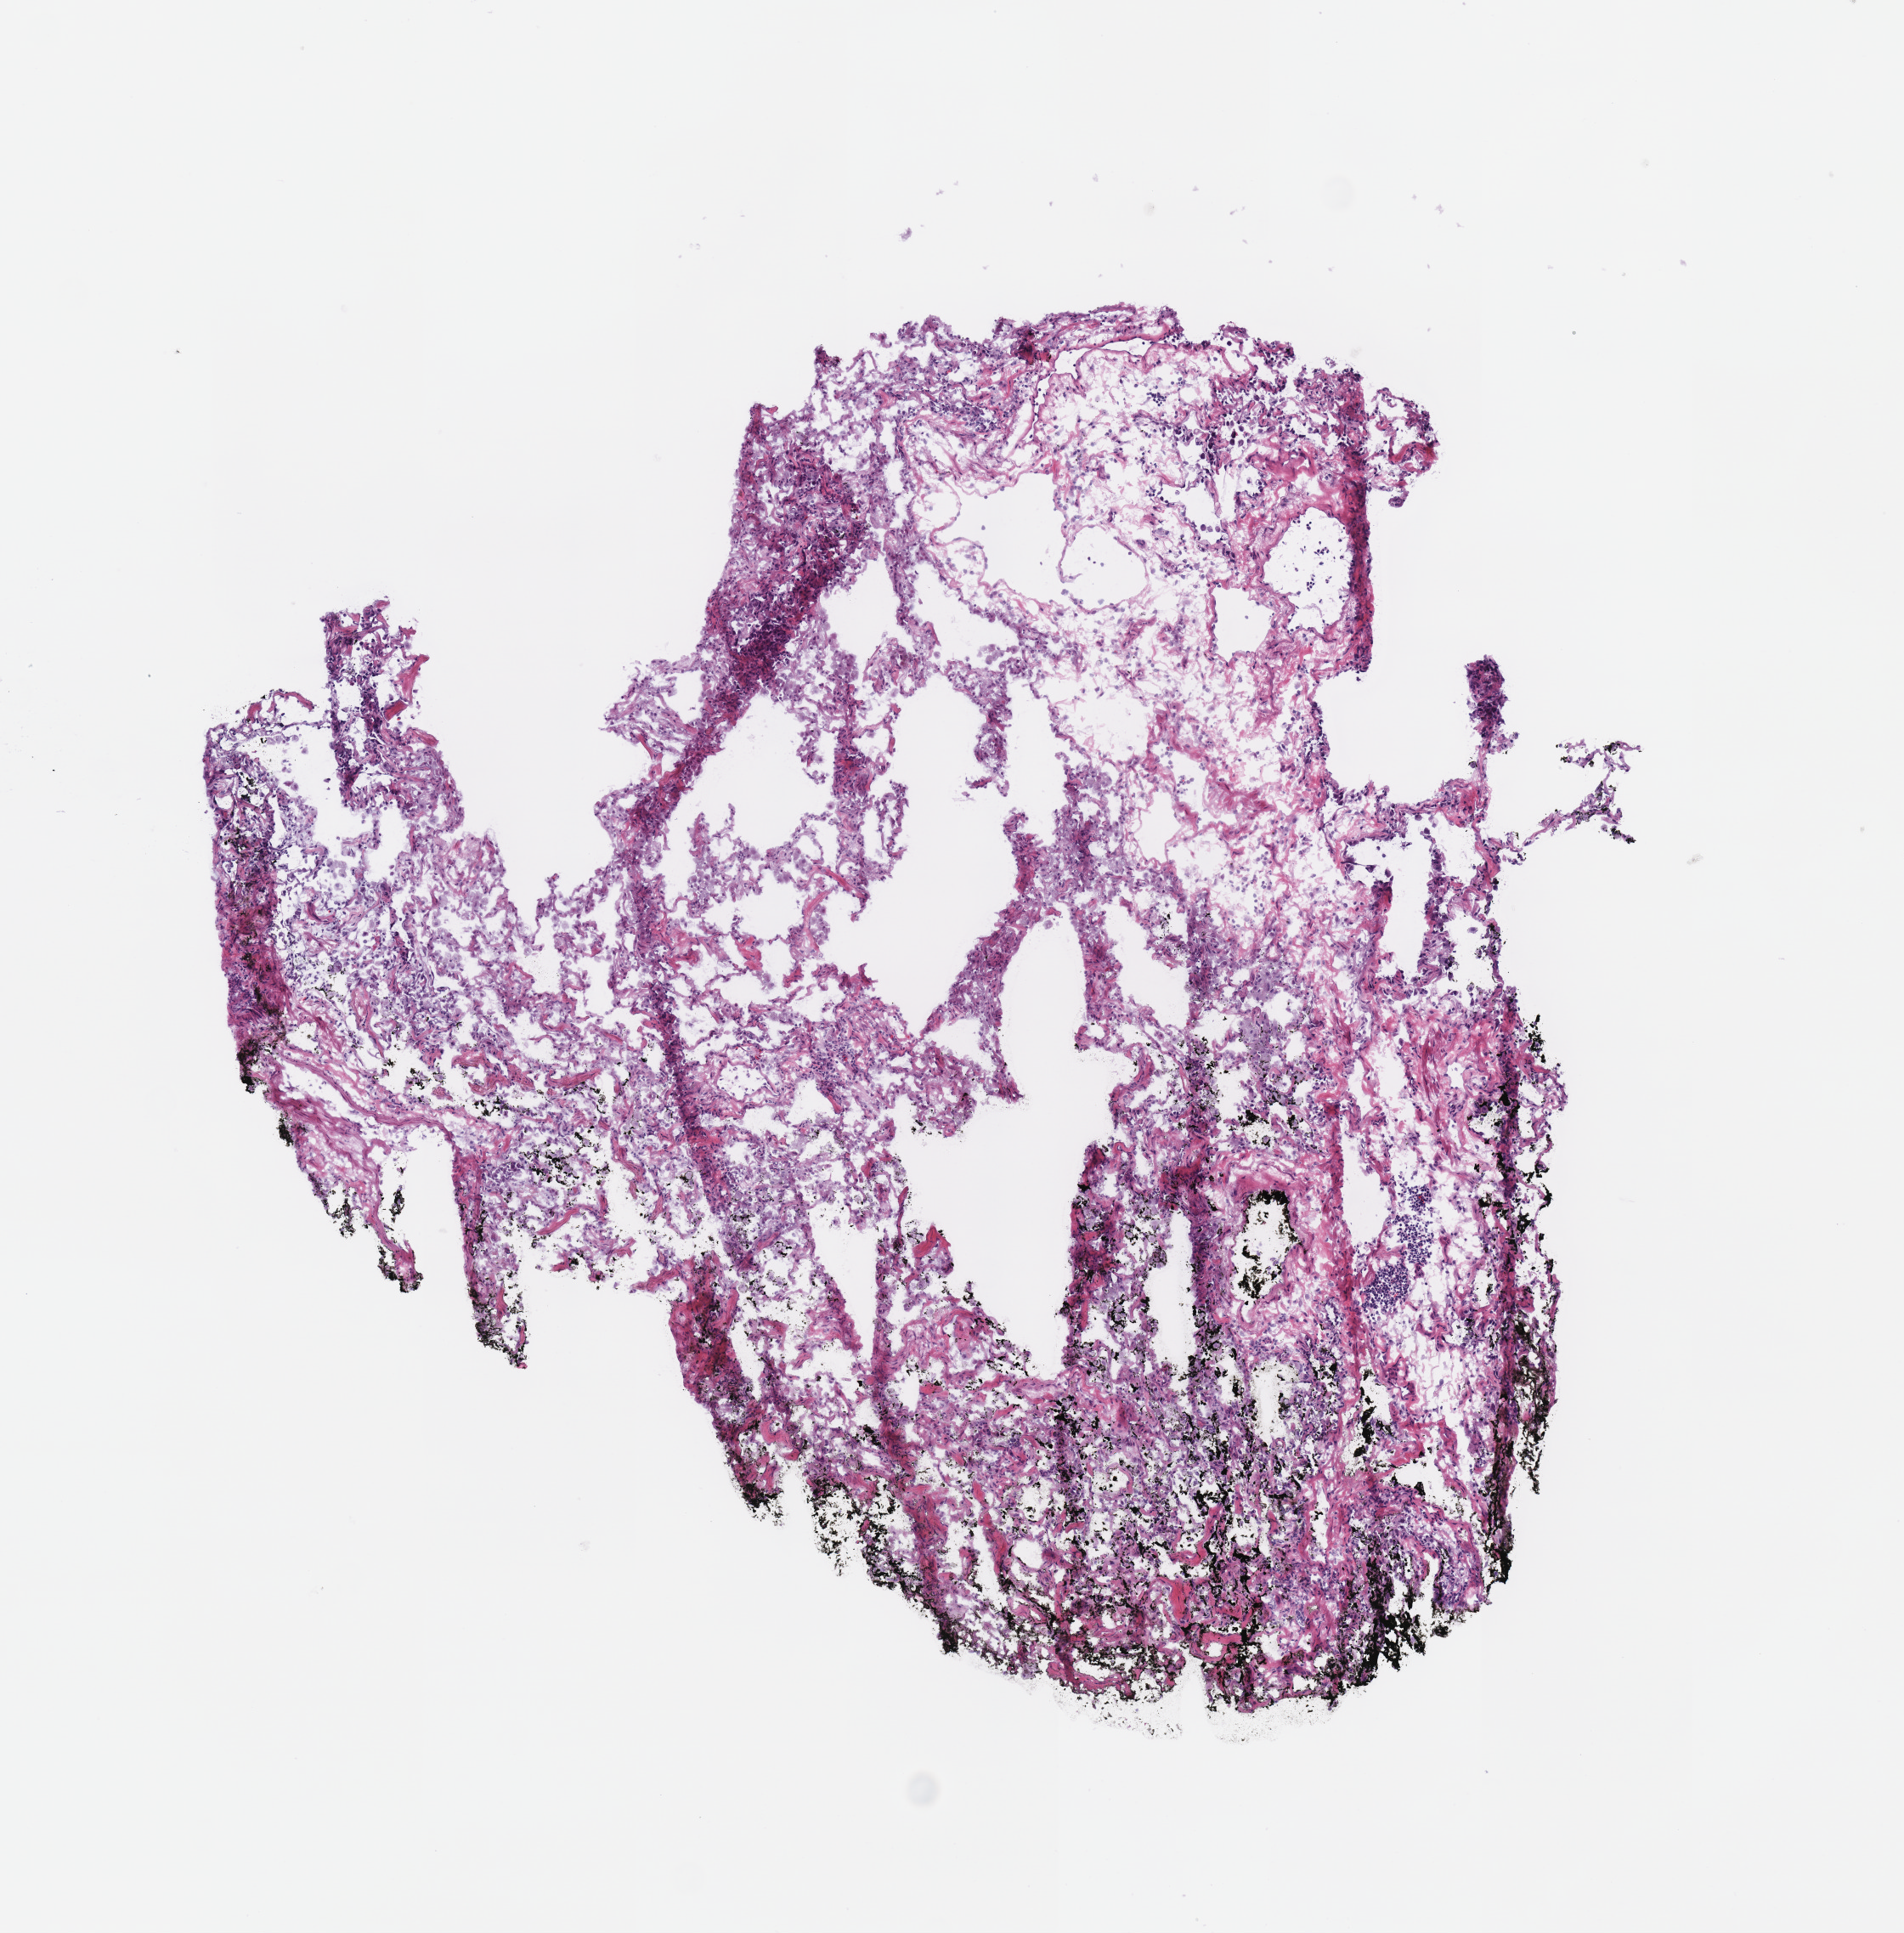
Digitized H&E tissue section (whole slide), a low-resolution overview of the entire scanned area, about 4.4 x 4.5 mm (acquisition: 40x scan); frozen section; sample: solid tissue normal (non-tumour tissue), lung. Female patient; age at initial diagnosis 66 years.
- this section: solid tissue normal (non-tumour) sample from the same patient
- patient diagnosis: Squamous cell carcinoma, NOS (lower lobe, lung)